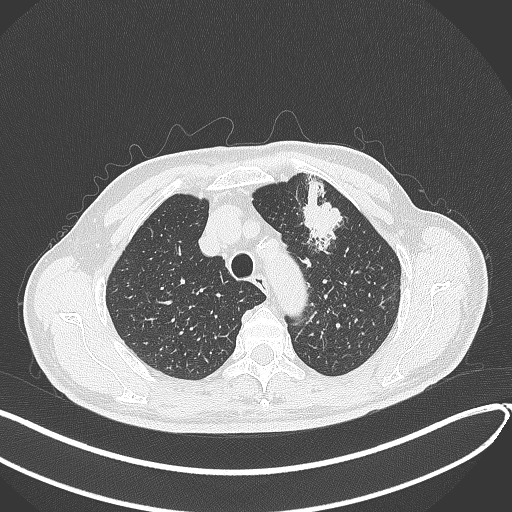
Chest CT, one axial slice; slice 335 of 459 in the series (ordered by position); reconstruction kernel B70f; 120 kVp; lung window (W 1500 / L -600 HU); 1 mm slice thickness; 512 × 512 image matrix, field of view 400 × 400 mm. Male patient, age 74 years. Case-level facts recorded for this patient, not image findings: clinical TNM (as recorded): T2b N0 M1c.
Outlined on this slice (rectangle marked by the reading radiologist):
- lung tumour (recorded histology: adenocarcinoma): bounding box <294,175,351,257> (left, top, right, bottom; pixels)